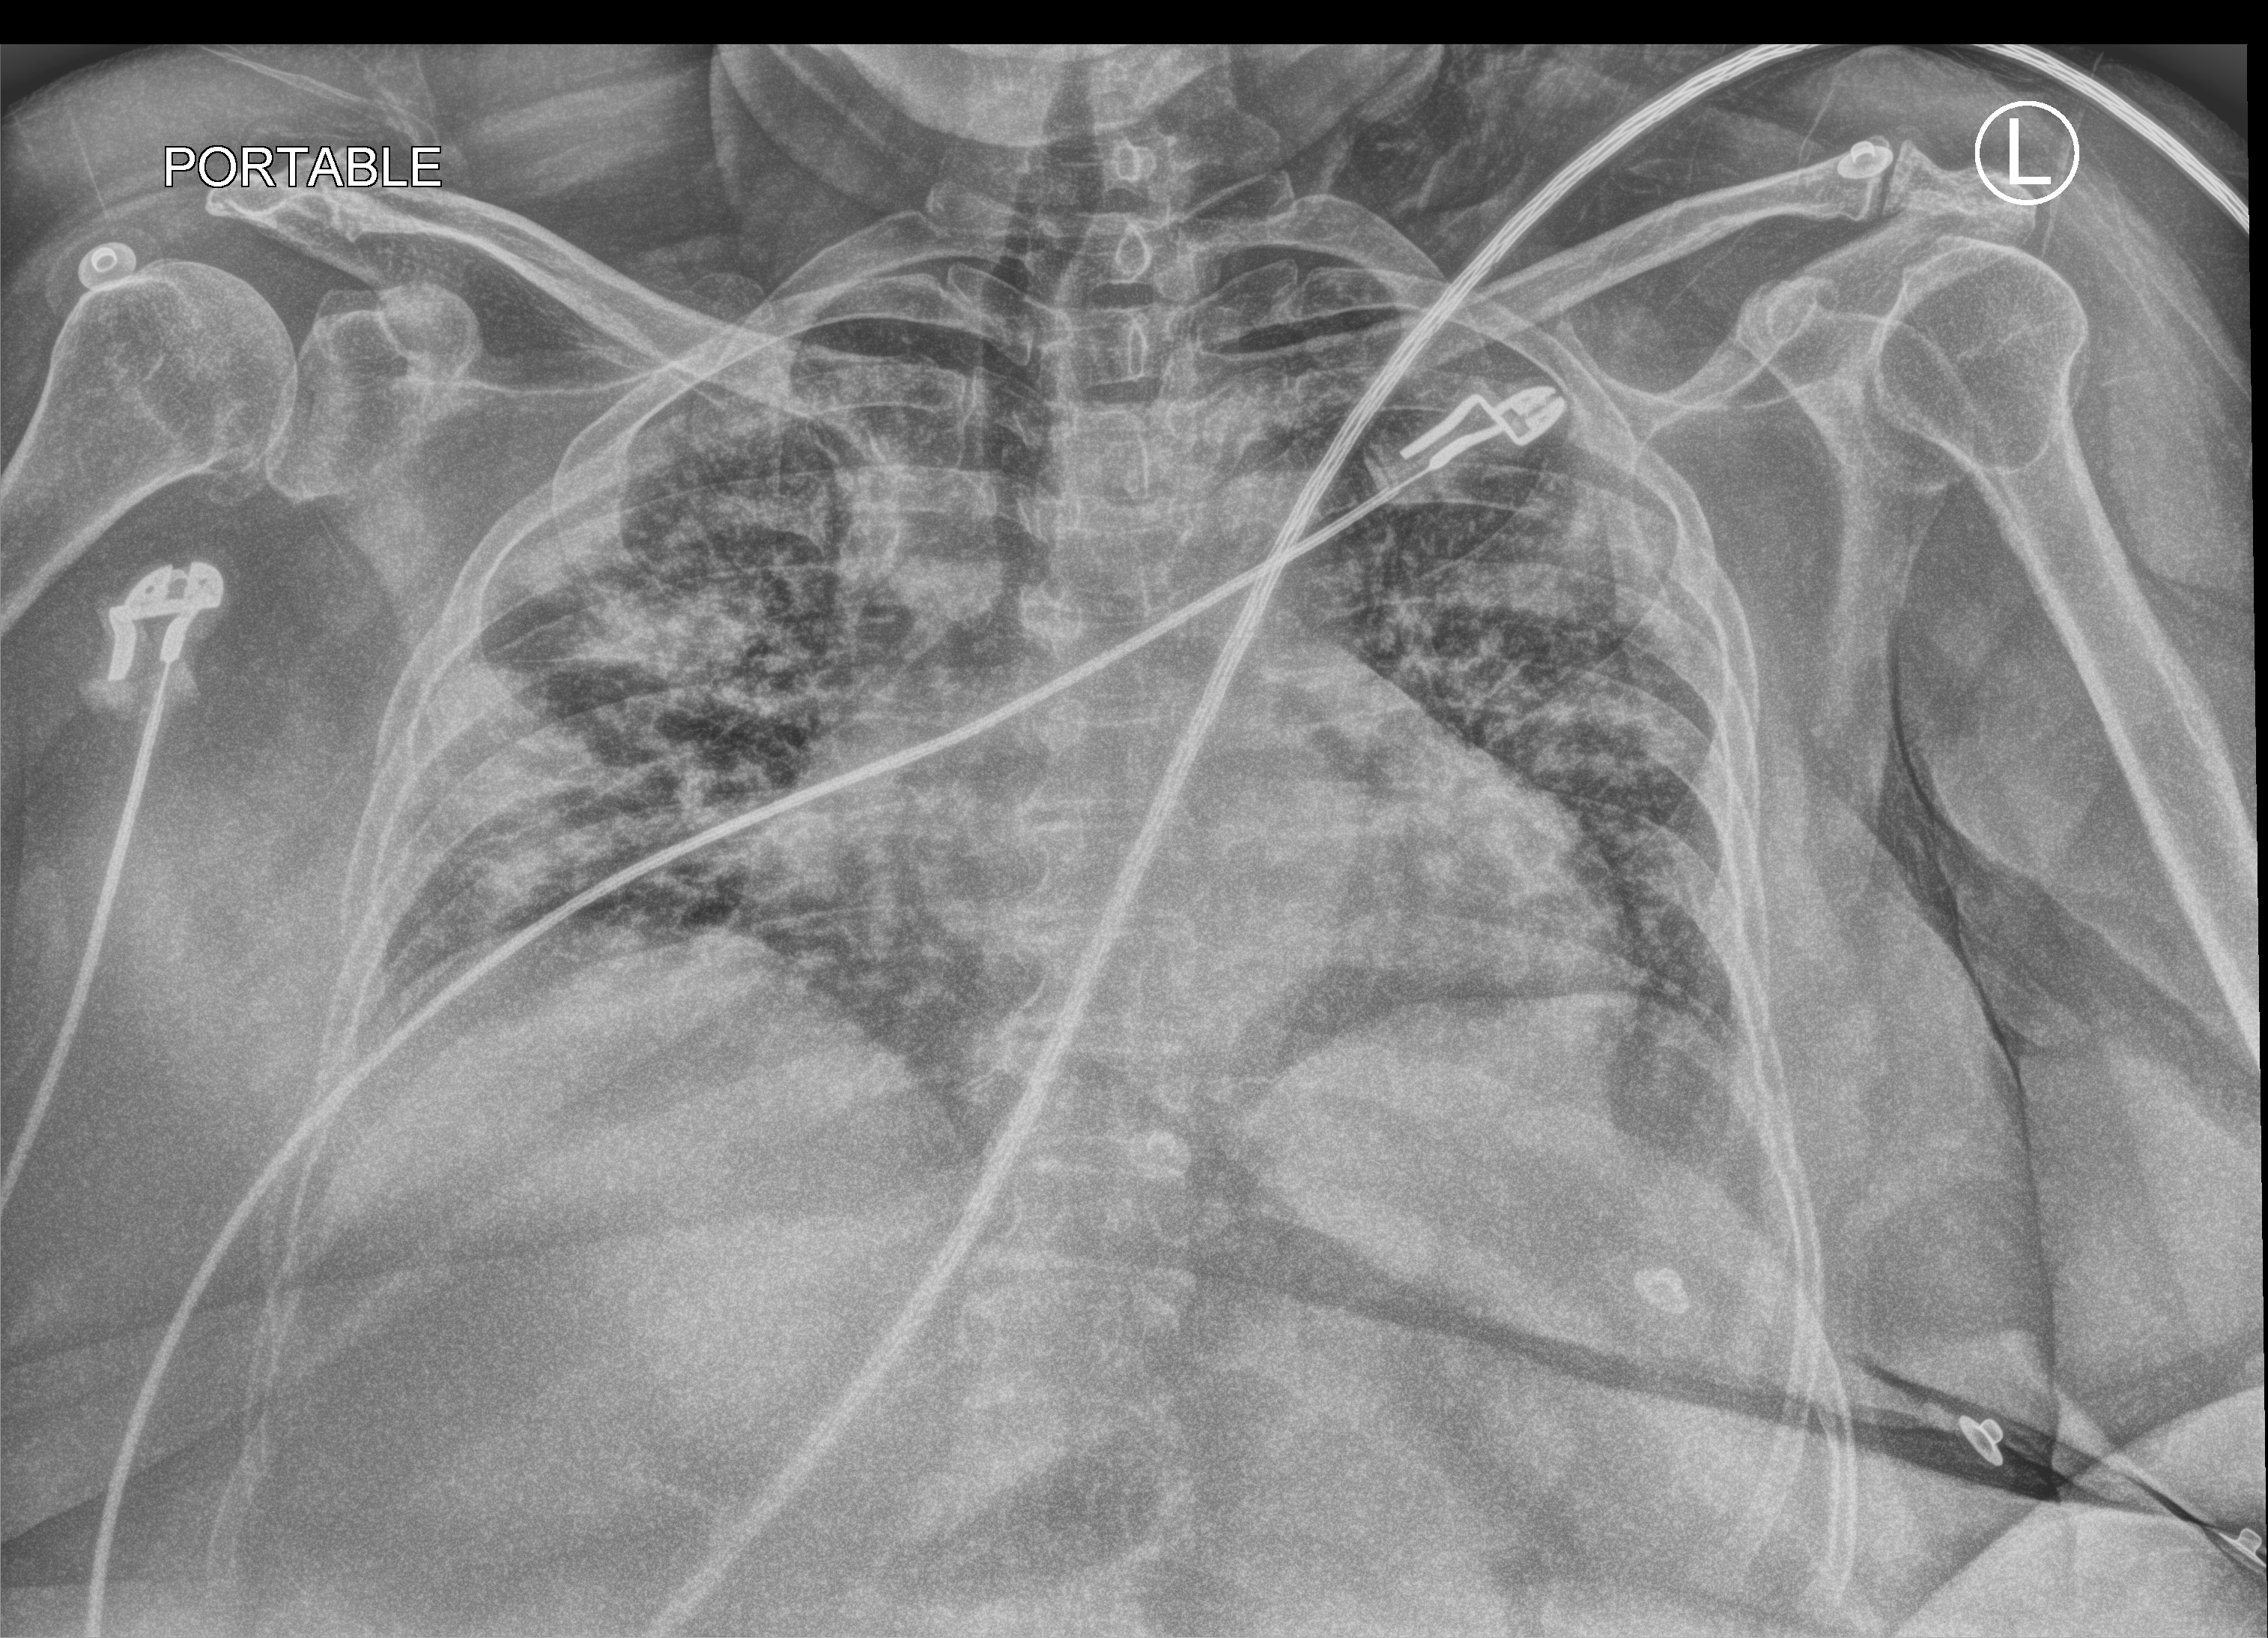
Portable chest radiograph. Patient hospitalised with COVID-19; female, aged 60–74 years.
From the hospital-stay record, not from the radiograph (when in the stay this image was taken is not recorded): hypertension (admission record): yes; mechanically ventilated during this hospital stay: no; admitted to intensive care during this hospital stay: no.